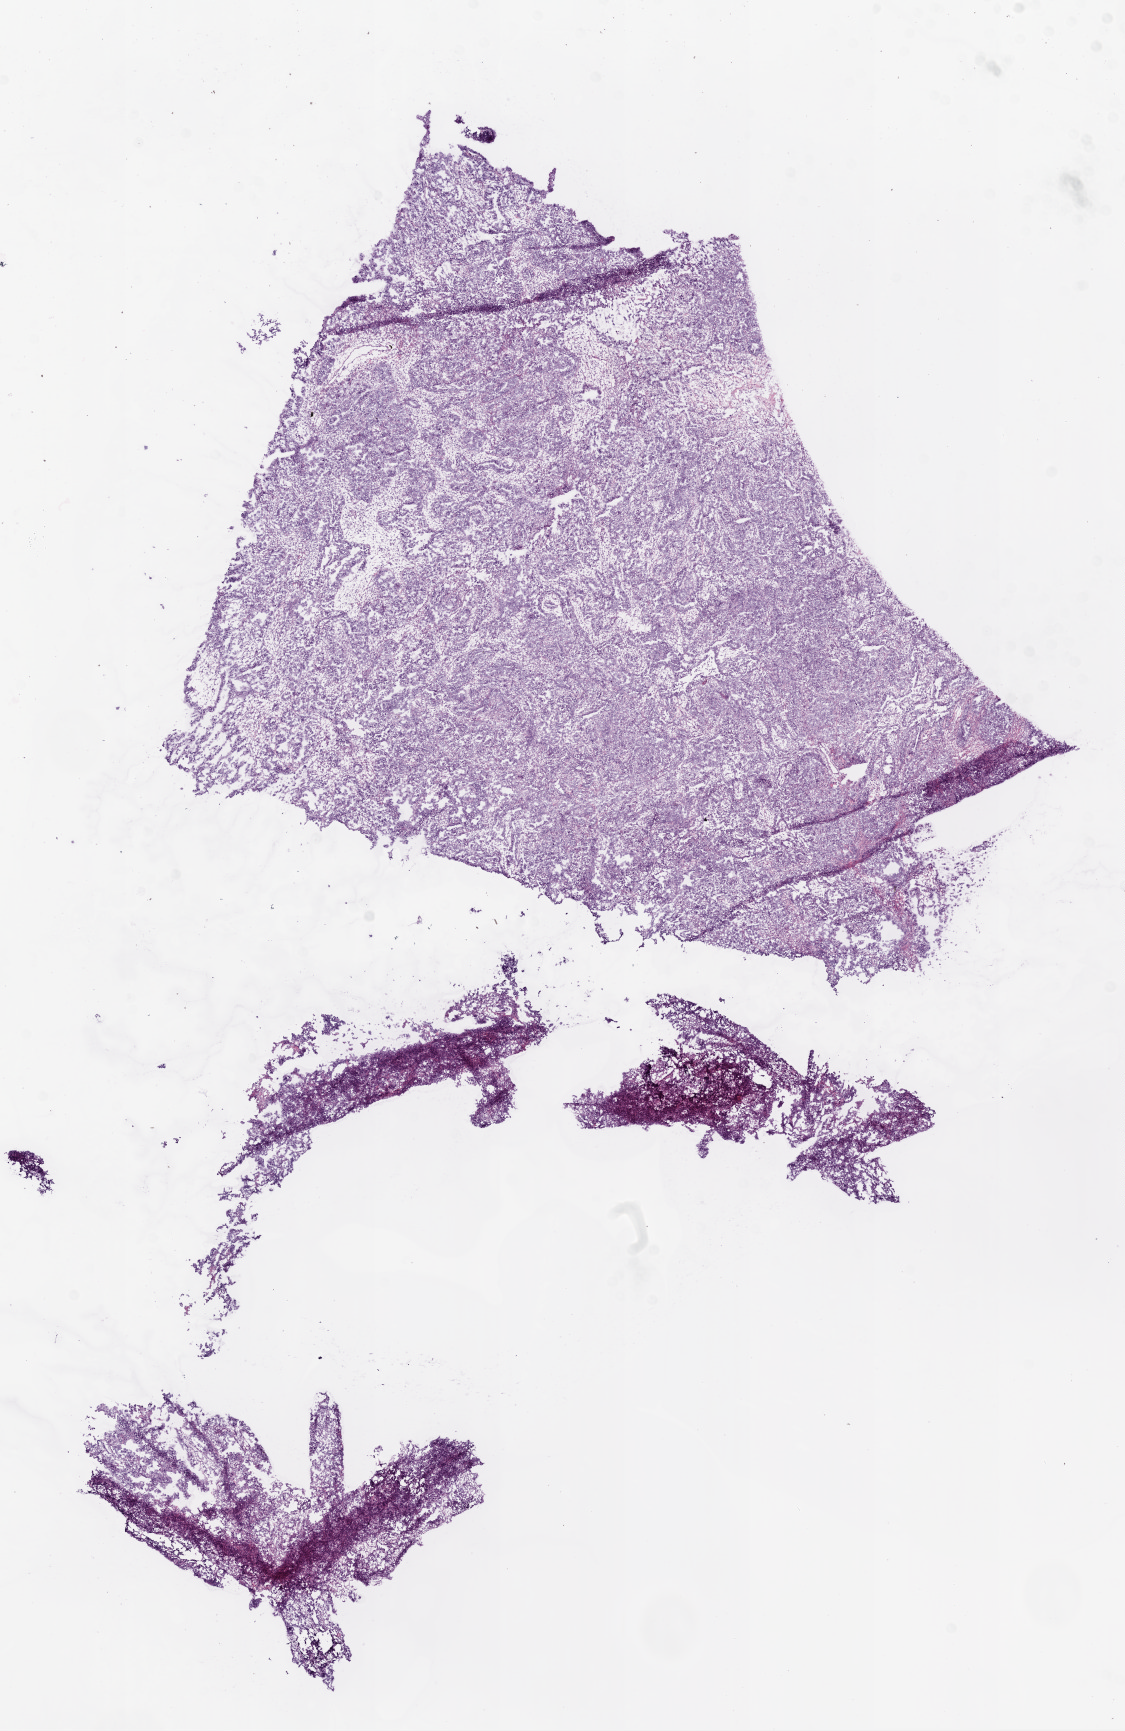
H&E whole-slide image — low-resolution overview of the scanned area, about 9.0 x 13.9 mm; frozen section; ovary, primary tumour sample. Female patient; age at initial diagnosis 45 years. Histologic grade: G3 (poorly differentiated). Composition of this section per pathologist review: tumour cells 95%, tumour nuclei 95%, normal cells 0%, stromal cells 5%, necrosis 0%.
Pathologic diagnosis: Serous cystadenocarcinoma, NOS. FIGO stage: IIIC.